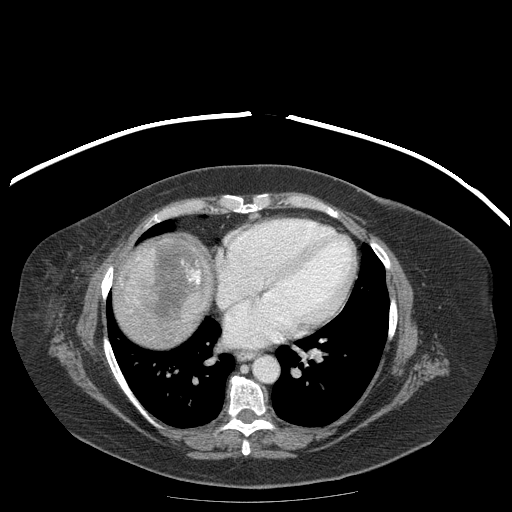
Contrast-enhanced abdominal CT (liver protocol), one axial slice; slice 177 of 204 in the series (ordered by position); reconstruction kernel STANDARD; soft-tissue window (W 400 / L 40 HU); 2.5 mm slice thickness; 512 × 512 image matrix. Case-level facts recorded for this patient, not image findings: diagnosis: hepatocellular carcinoma (patient treated with transarterial chemoembolisation; whether this scan precedes or follows treatment is not stated here); TNM stage (as recorded): Stage-IIIB; Child-Pugh class: A; tumour differentiation: well differentiated; tumour nodularity: uninodular.
Structures marked on this image (semi-automatic segmentation, software-assisted and operator-edited):
- liver parenchyma outside the tumour (the mass and vessels are separate outlines, so this box may not span the whole liver): bounding box <114,235,211,346> (left, top, right, bottom; pixels)
- mass: <124,238,205,321>